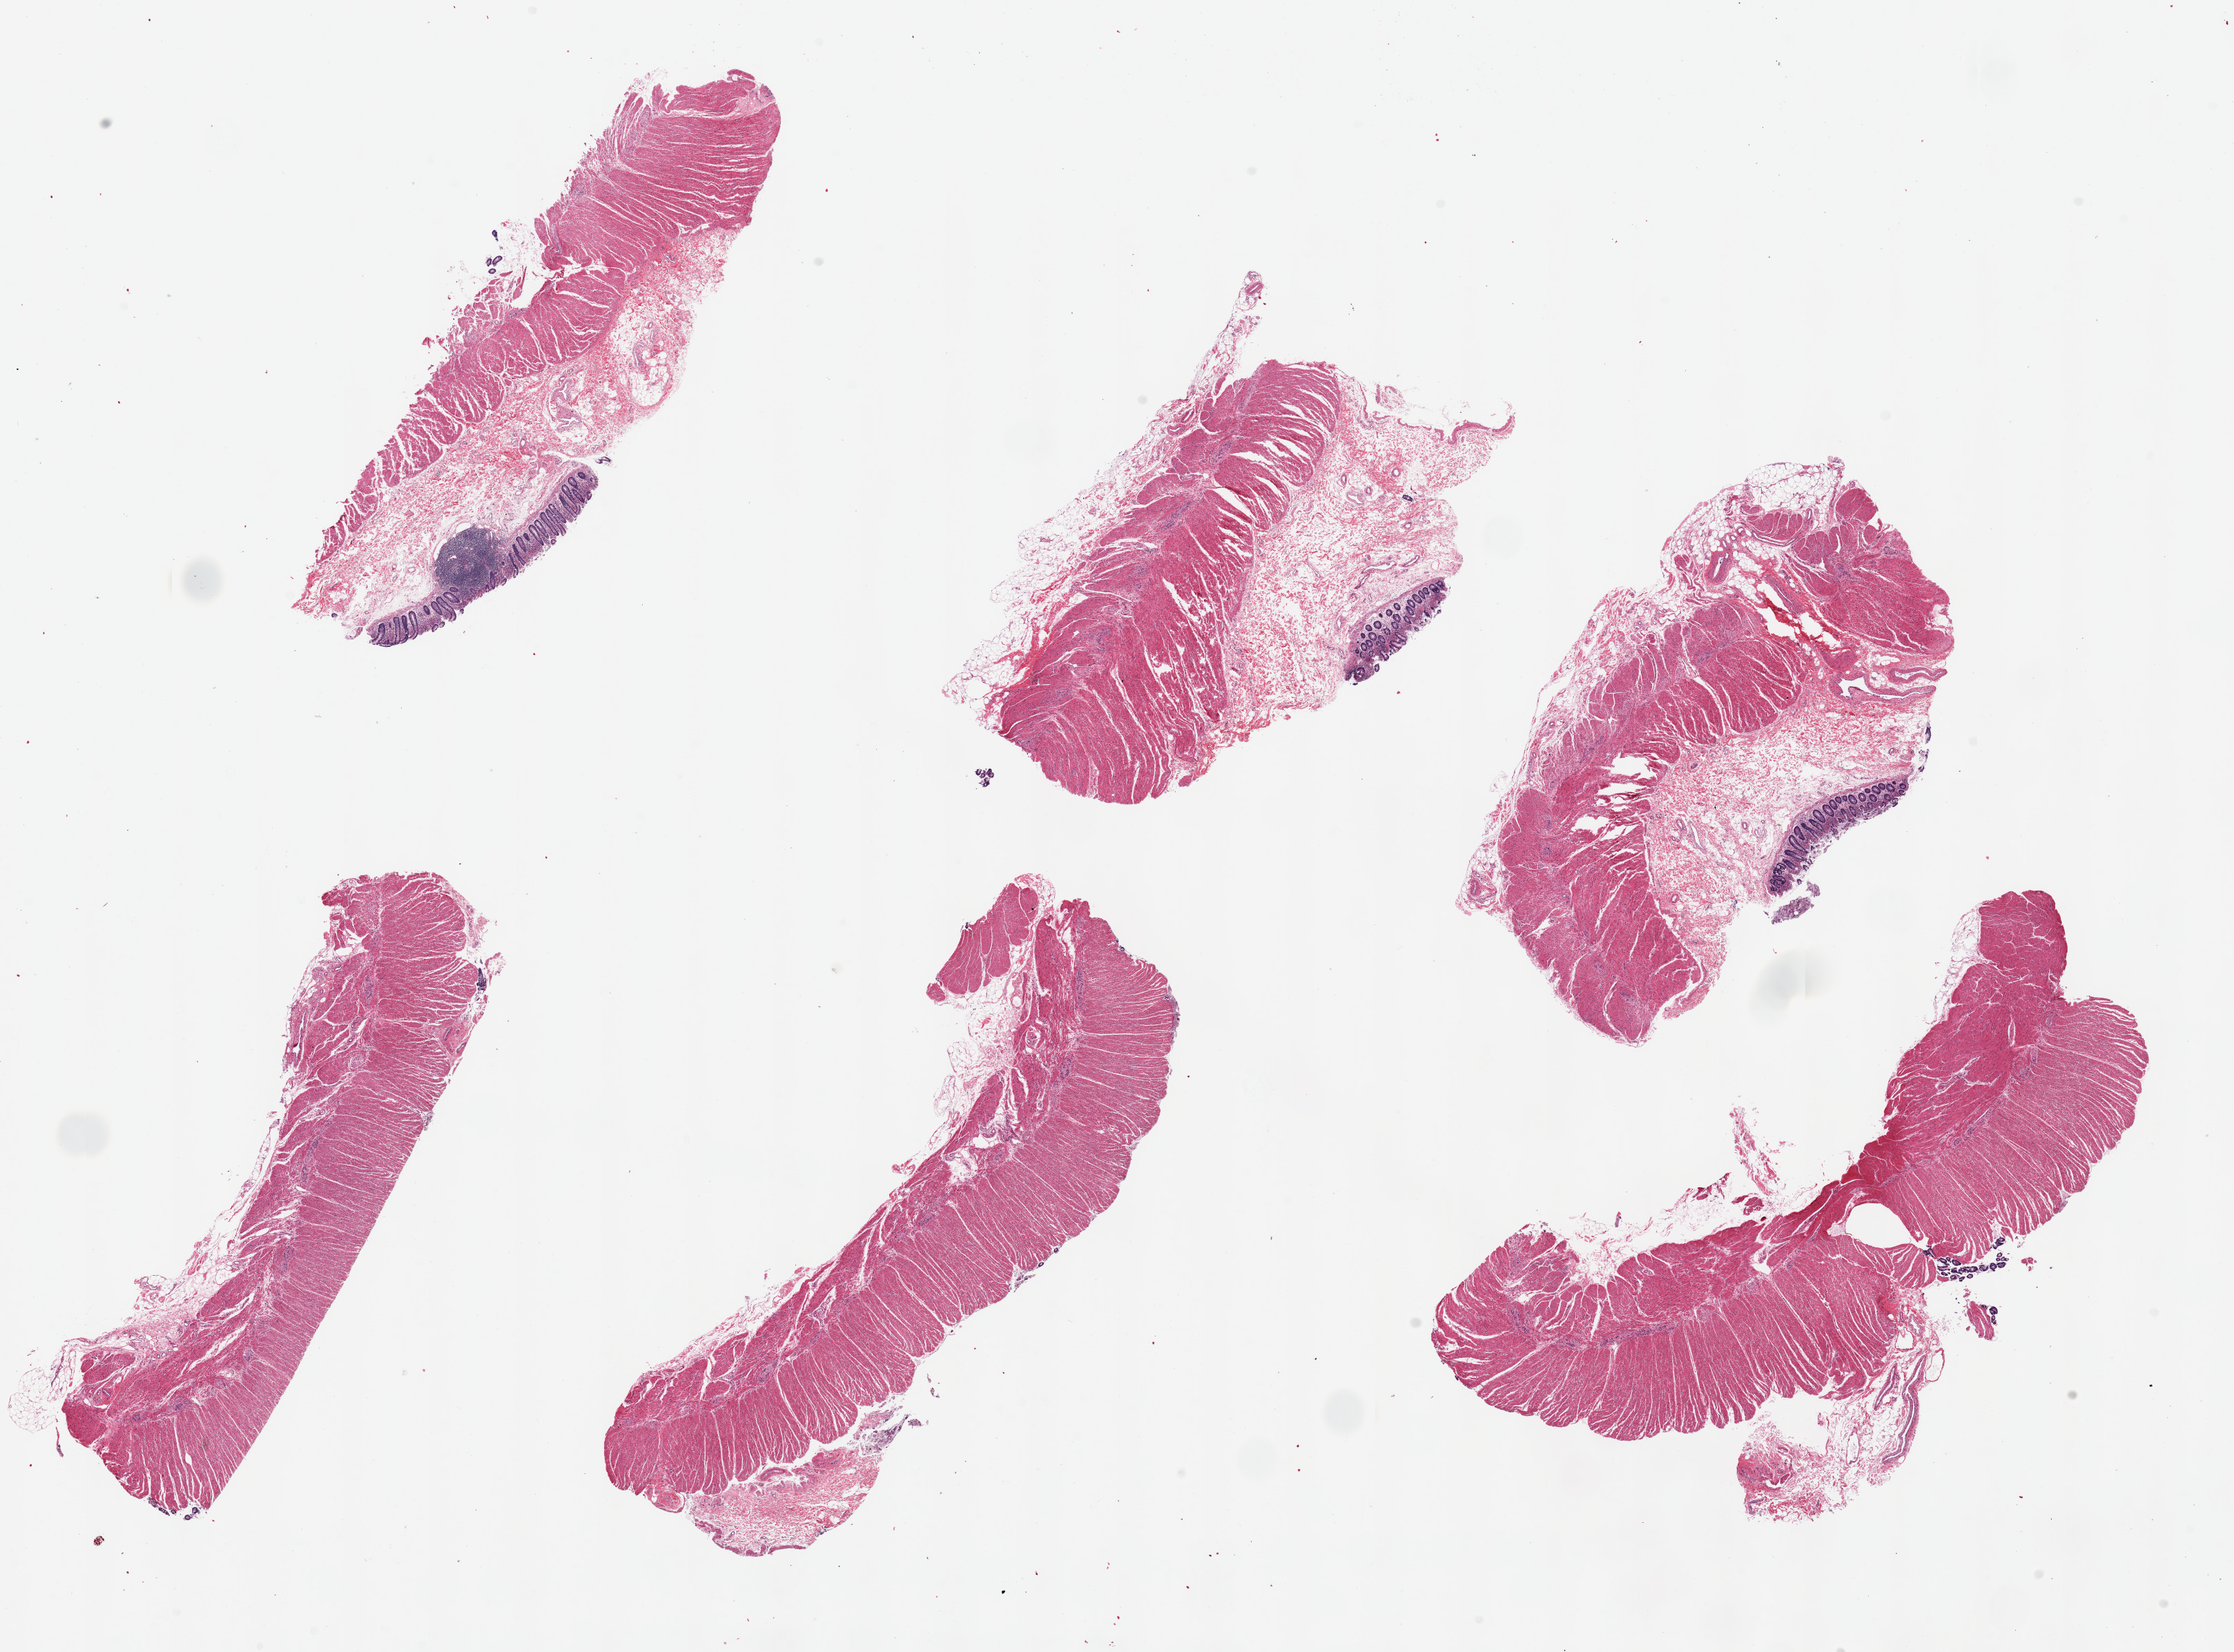
Hematoxylin and eosin (H&E) whole-slide image, low-resolution overview of the scanned area, about 25.6 x 18.9 mm; PAXgene-fixed, paraffin-embedded tissue; target tissue: sigmoid colon; donor tissue sample. Male donor.
• review note (as recorded): 6 pieces ~8x2mm; All muscle in 3; contaminant mucosa is 3